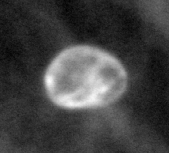
Region of interest cut from a scanned film mammogram (one marked finding), left breast, MLO view, BI-RADS breast density category 1 (scale 1–4).
Marked abnormality: calcifications, morphology eggshell; BI-RADS assessment category 2; subtlety rating 5 on a 1 (subtle) to 5 (obvious) scale; benign without callback (not worked up further).